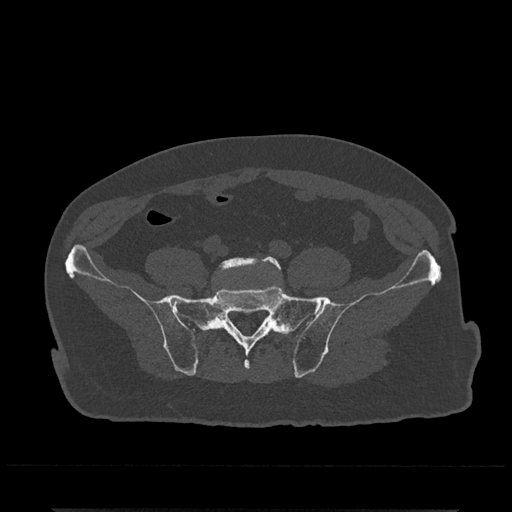
CT including the spine, one axial slice. Position 38 of 797 along the scan axis. Bone window (W 1800 / L 400 HU). 0.5 mm slice thickness. 512 × 512 image matrix, field of view 393 × 393 mm. Patient: male, 67 years. Case-level facts recorded for this patient, not image findings: primary cancer: prostate.
Annotated regions visible in this slice (semi-automatically segmented with operator editing):
- L5 vertebra: bounding box (x1, y1, x2, y2) in pixels: (217, 256, 282, 277)